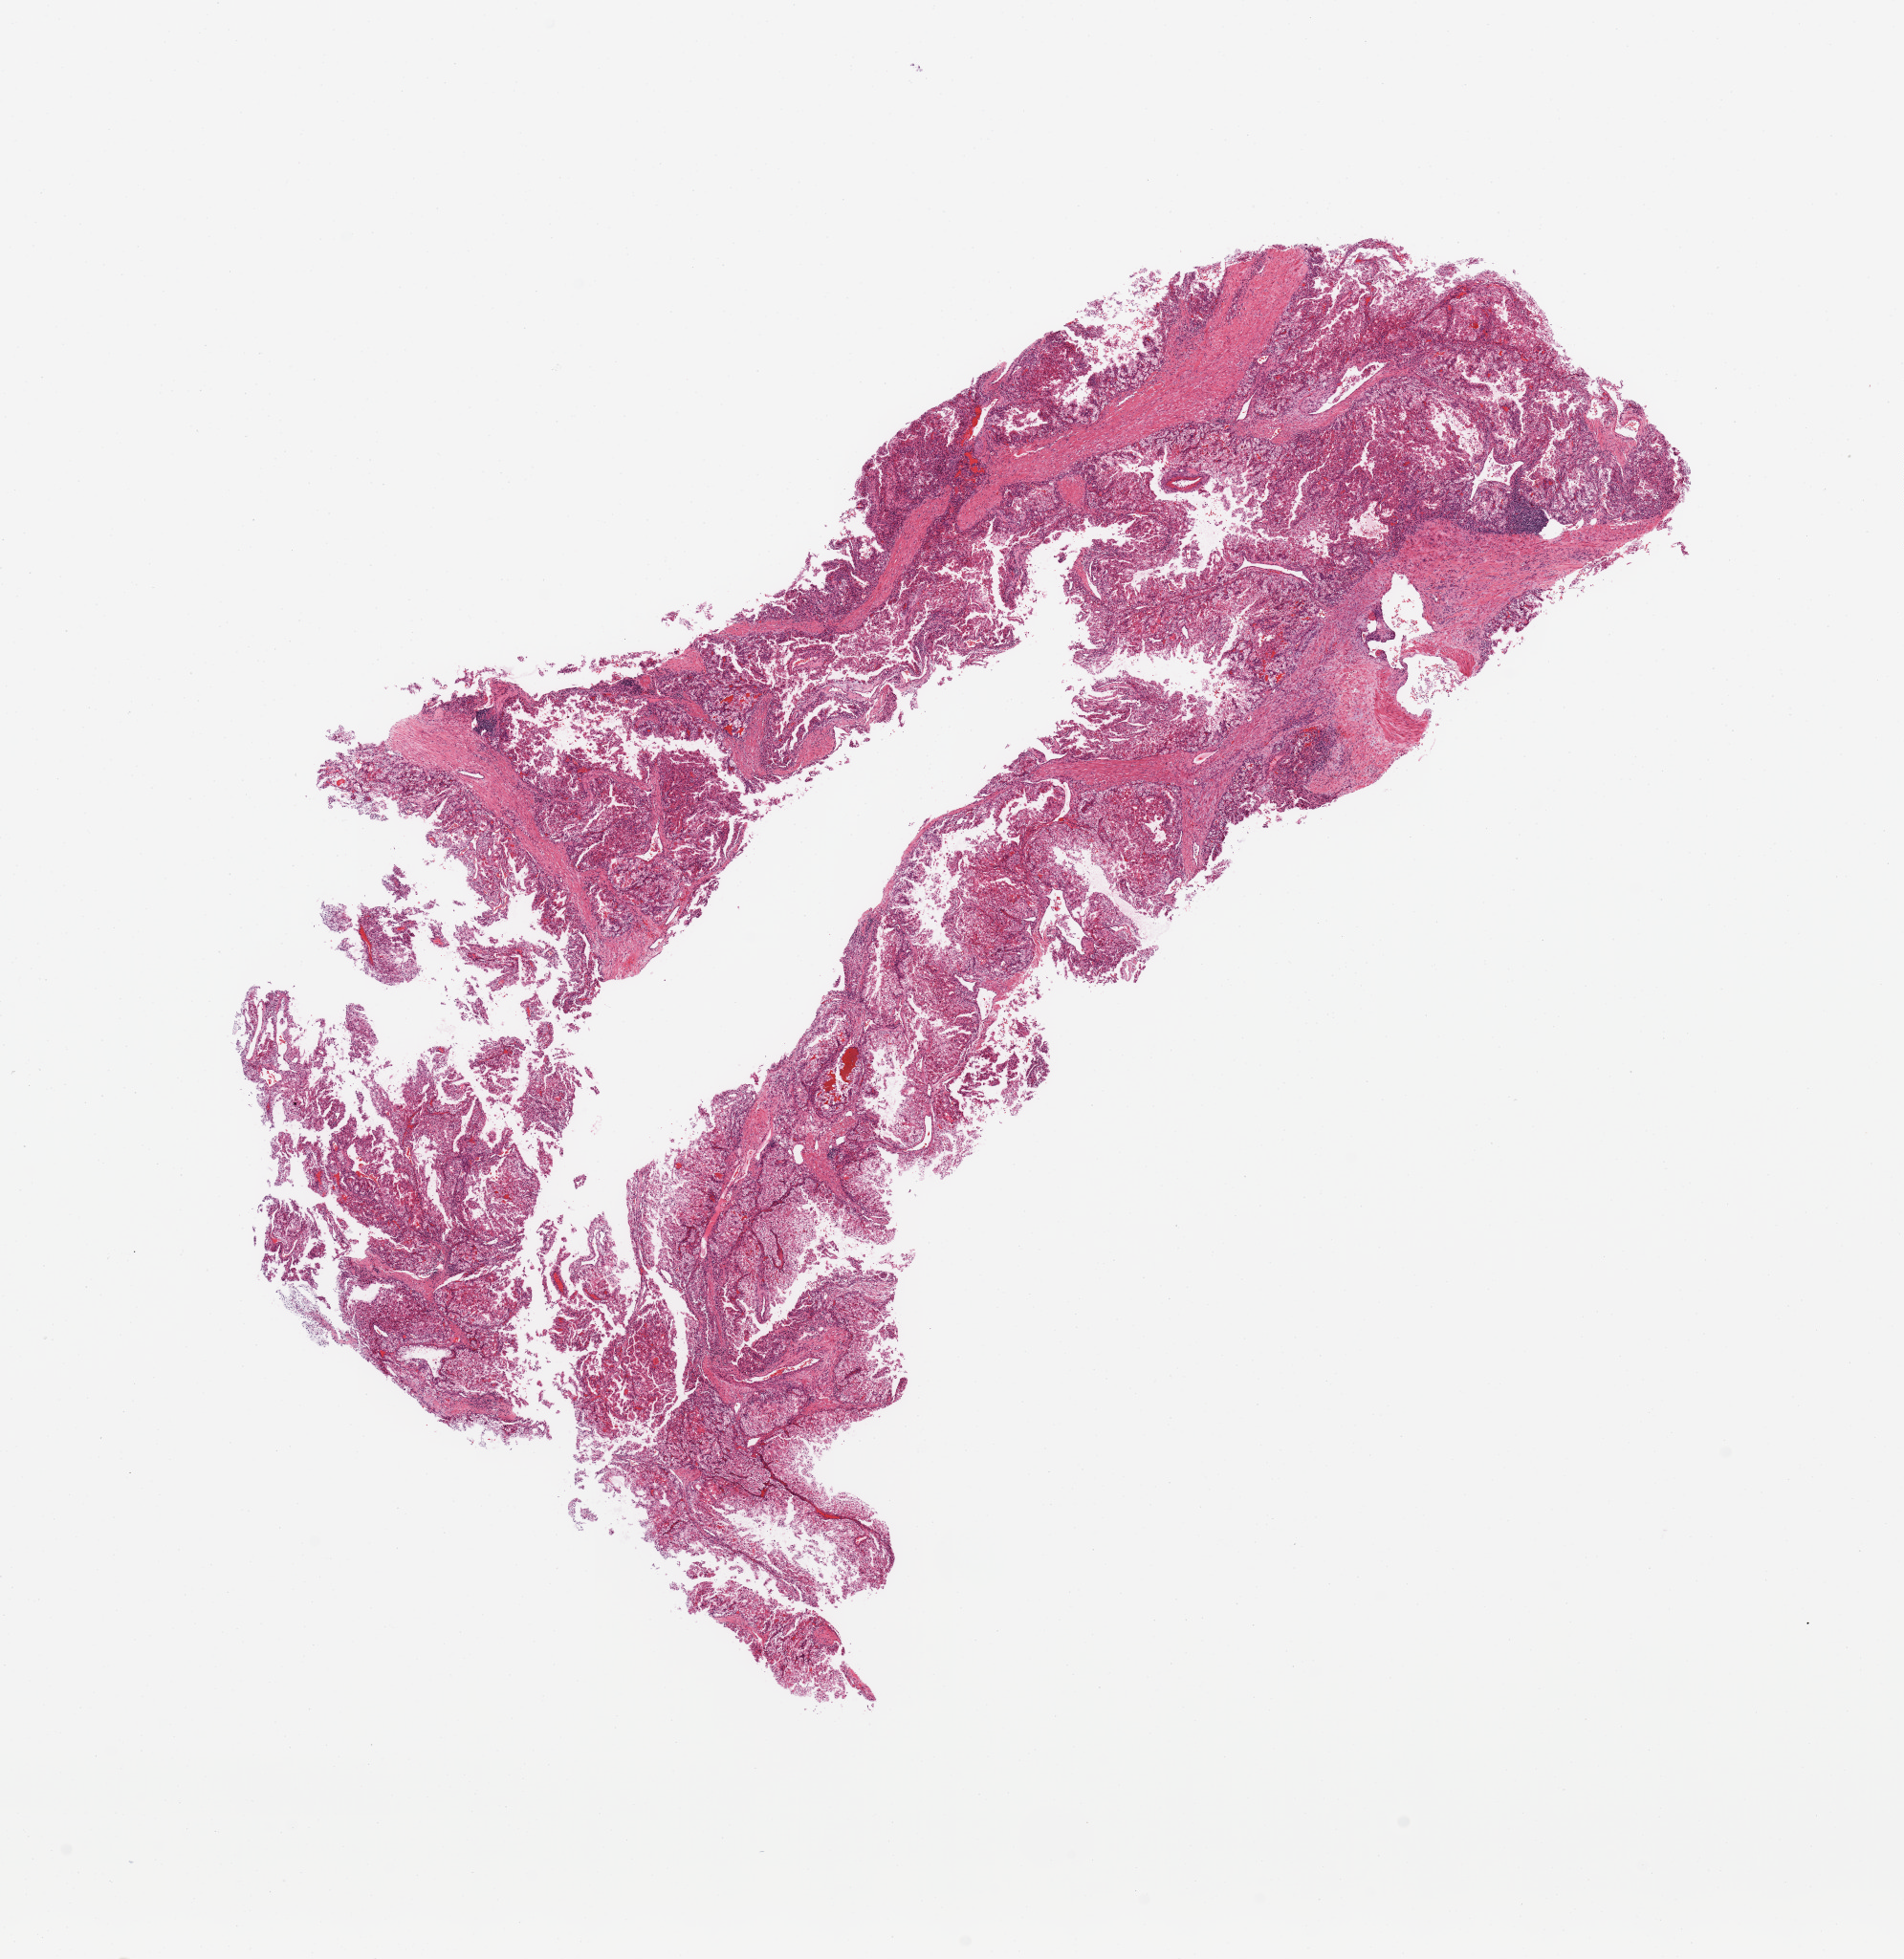
H&E whole-slide image — whole scanned area (about 15.8 x 16.2 mm, slide scanned at 20x) shown as a low-resolution overview. Tumour tissue sample, sampled site: kidney. 52-year-old male patient. Histologic grade: G2 (moderately differentiated). Composition of this section per pathologist review: tumour nuclei 80%, necrosis 0%.
- histologic diagnosis: Renal cell carcinoma, NOS
- AJCC pathologic stage: II